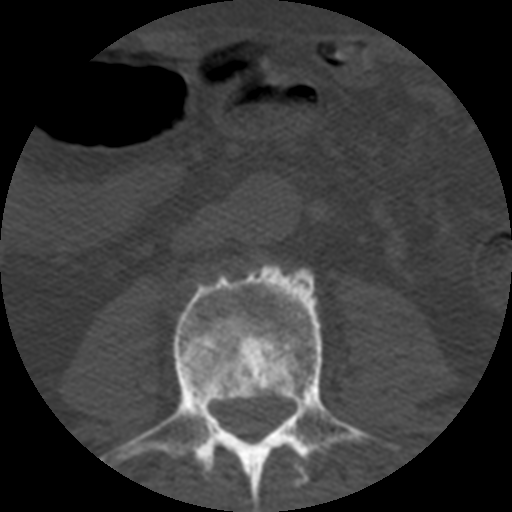
CT including the spine, one axial slice. Position 121 of 508 along the scan axis. Reconstruction kernel STANDARD. 120 kVp. Bone window (W 1800 / L 400 HU). 1.25 mm slice thickness. 512 × 512 image matrix. Patient age 57 years. From the clinical record (not read from this slice): primary cancer: prostate.
Structures marked on this image (semi-automatically segmented with operator editing):
- L2 vertebra: bounding box [x1, y1, x2, y2] px = [214, 443, 309, 488]
- L3 vertebra: [103, 263, 400, 509]